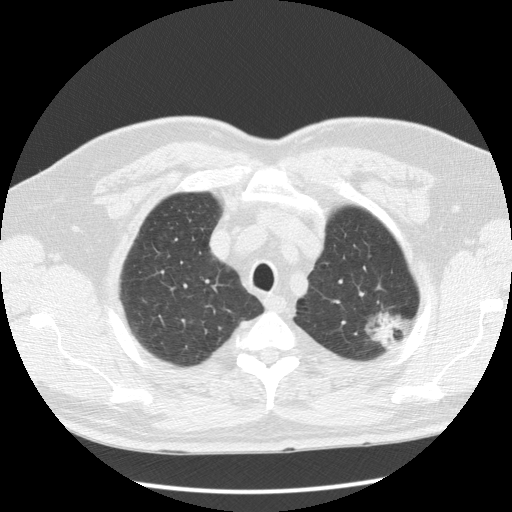
Low-dose screening chest CT, one axial slice. Position 104 of 123 along the scan axis. Reconstruction kernel STANDARD. 120 kVp. Lung window (W 1500 / L -600 HU). 512 × 512 image matrix, field of view 355 × 355 mm.
Annotated regions visible in this slice (expert manual segmentation):
- lesion 1 (tumor, upper lobe of left lung): bounding box (x1, y1, x2, y2) in pixels: (372, 315, 394, 343)